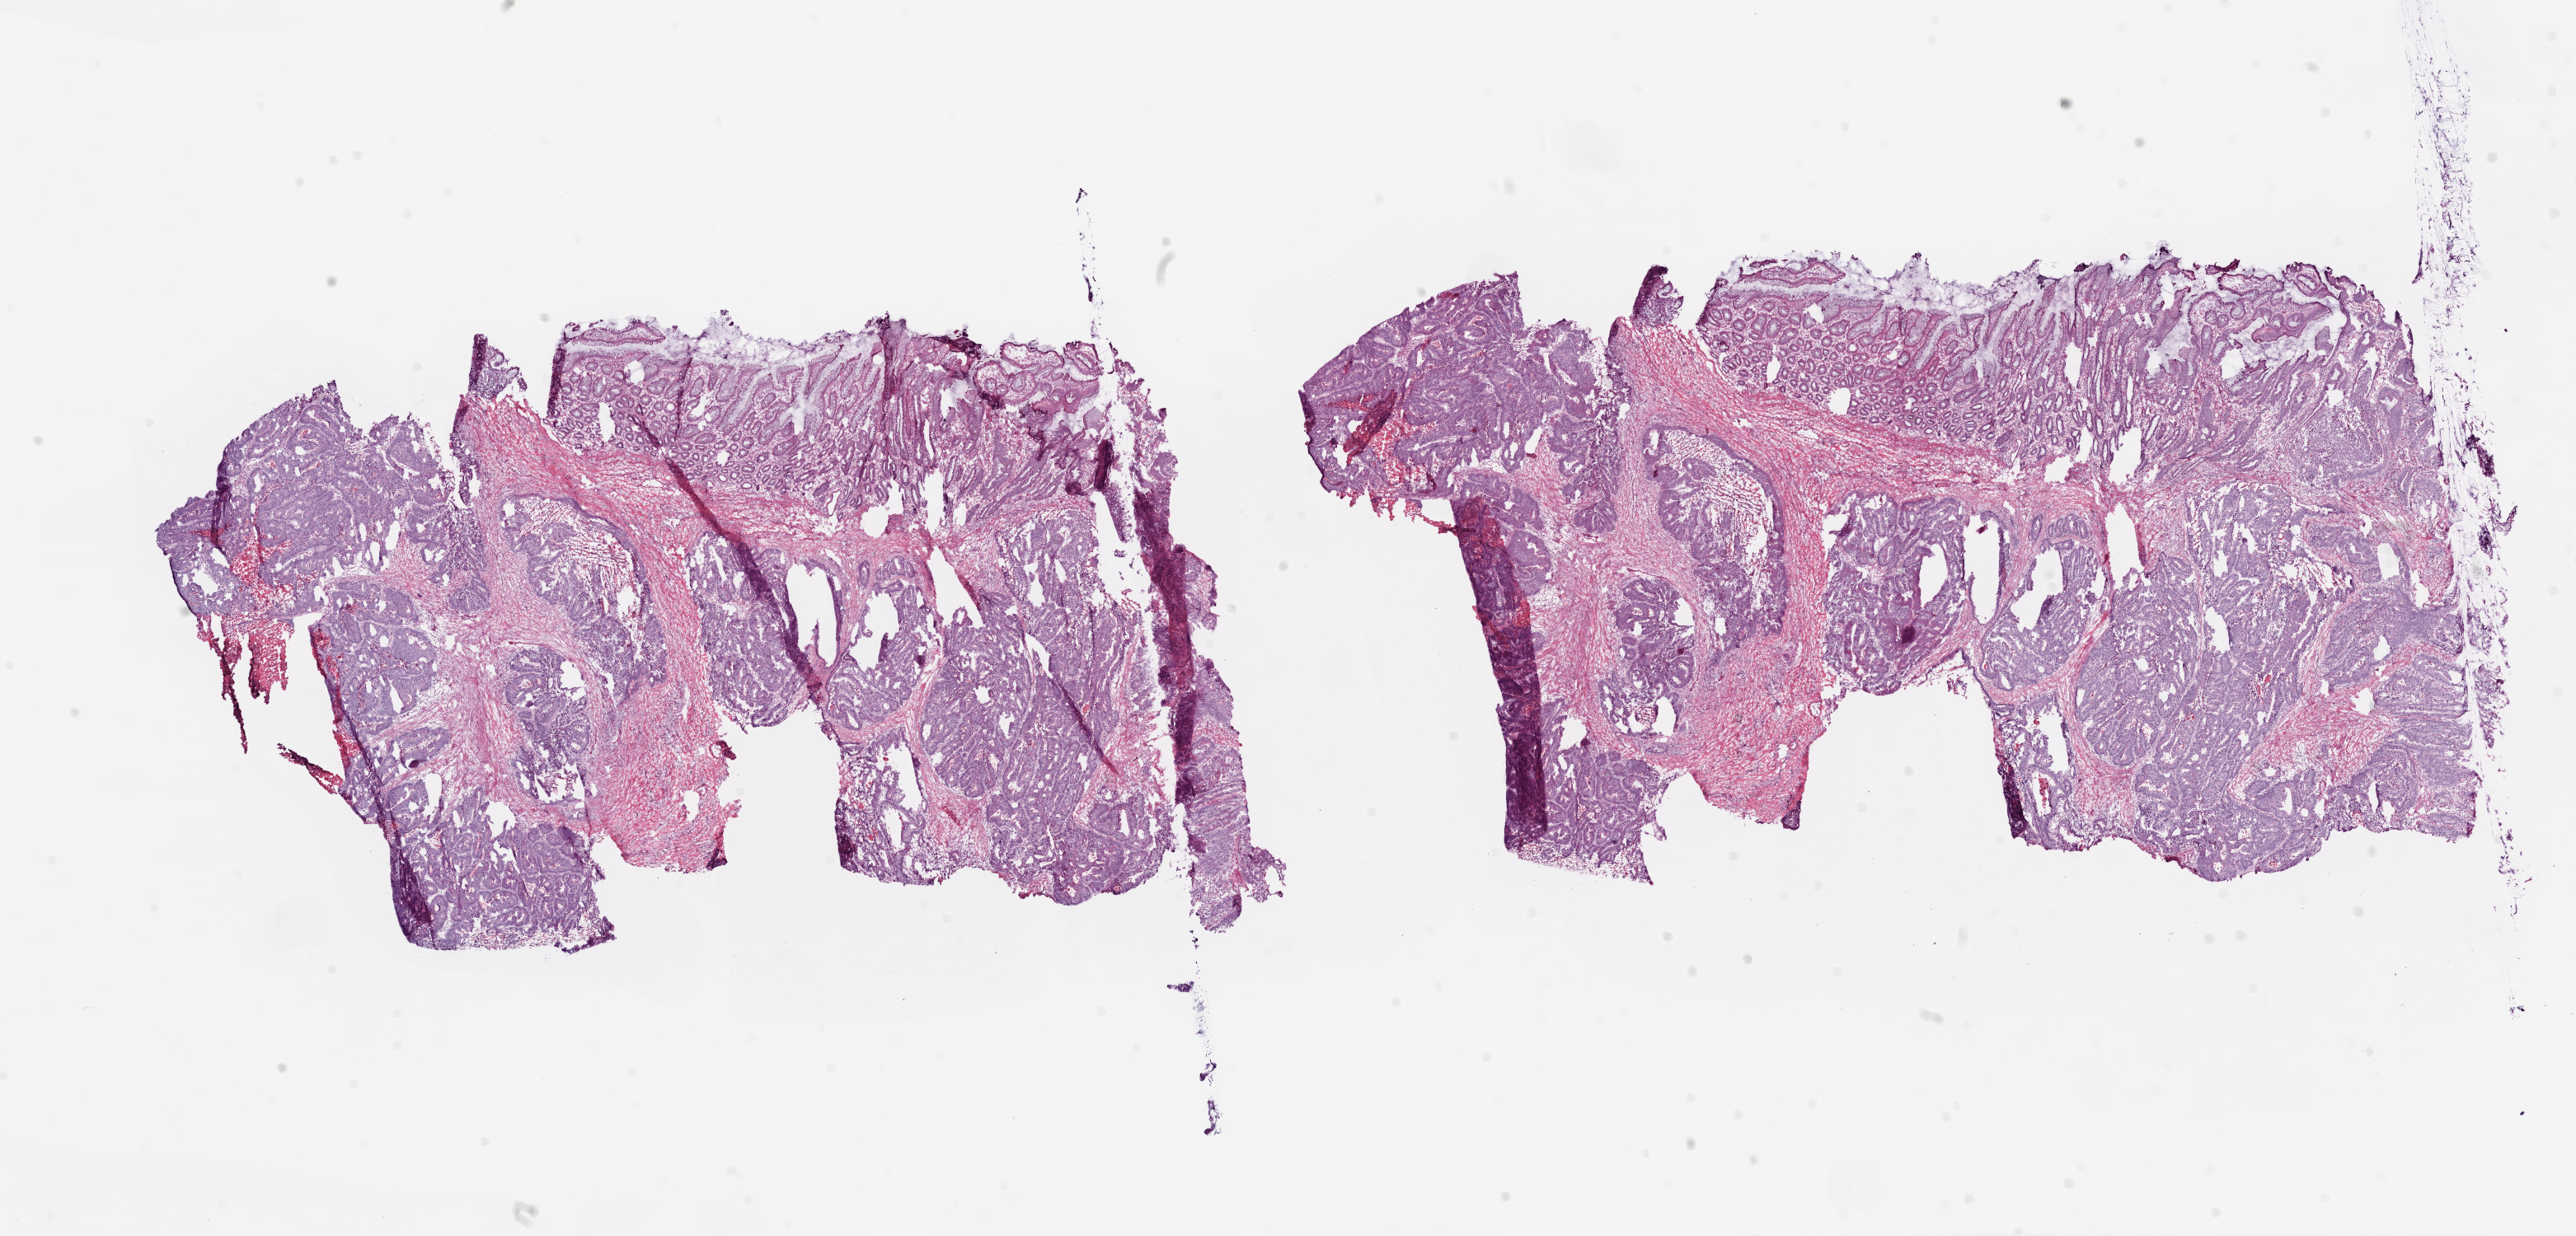
Whole-slide histology image, H&E — whole scanned area (about 25.1 x 12.0 mm, from a 20x scan) shown as a low-resolution overview; frozen section from the top of the tissue portion; primary tumour sample from the colon. Patient: female, age at initial diagnosis 75 years. Slide review estimates, as recorded: tumour cells 70%, tumour nuclei 80%, normal cells 10%, stromal cells 20%, necrosis 0%.
• AJCC pathologic stage: IIA (6th edition)
• histologic diagnosis: Adenocarcinoma, NOS (sigmoid colon)